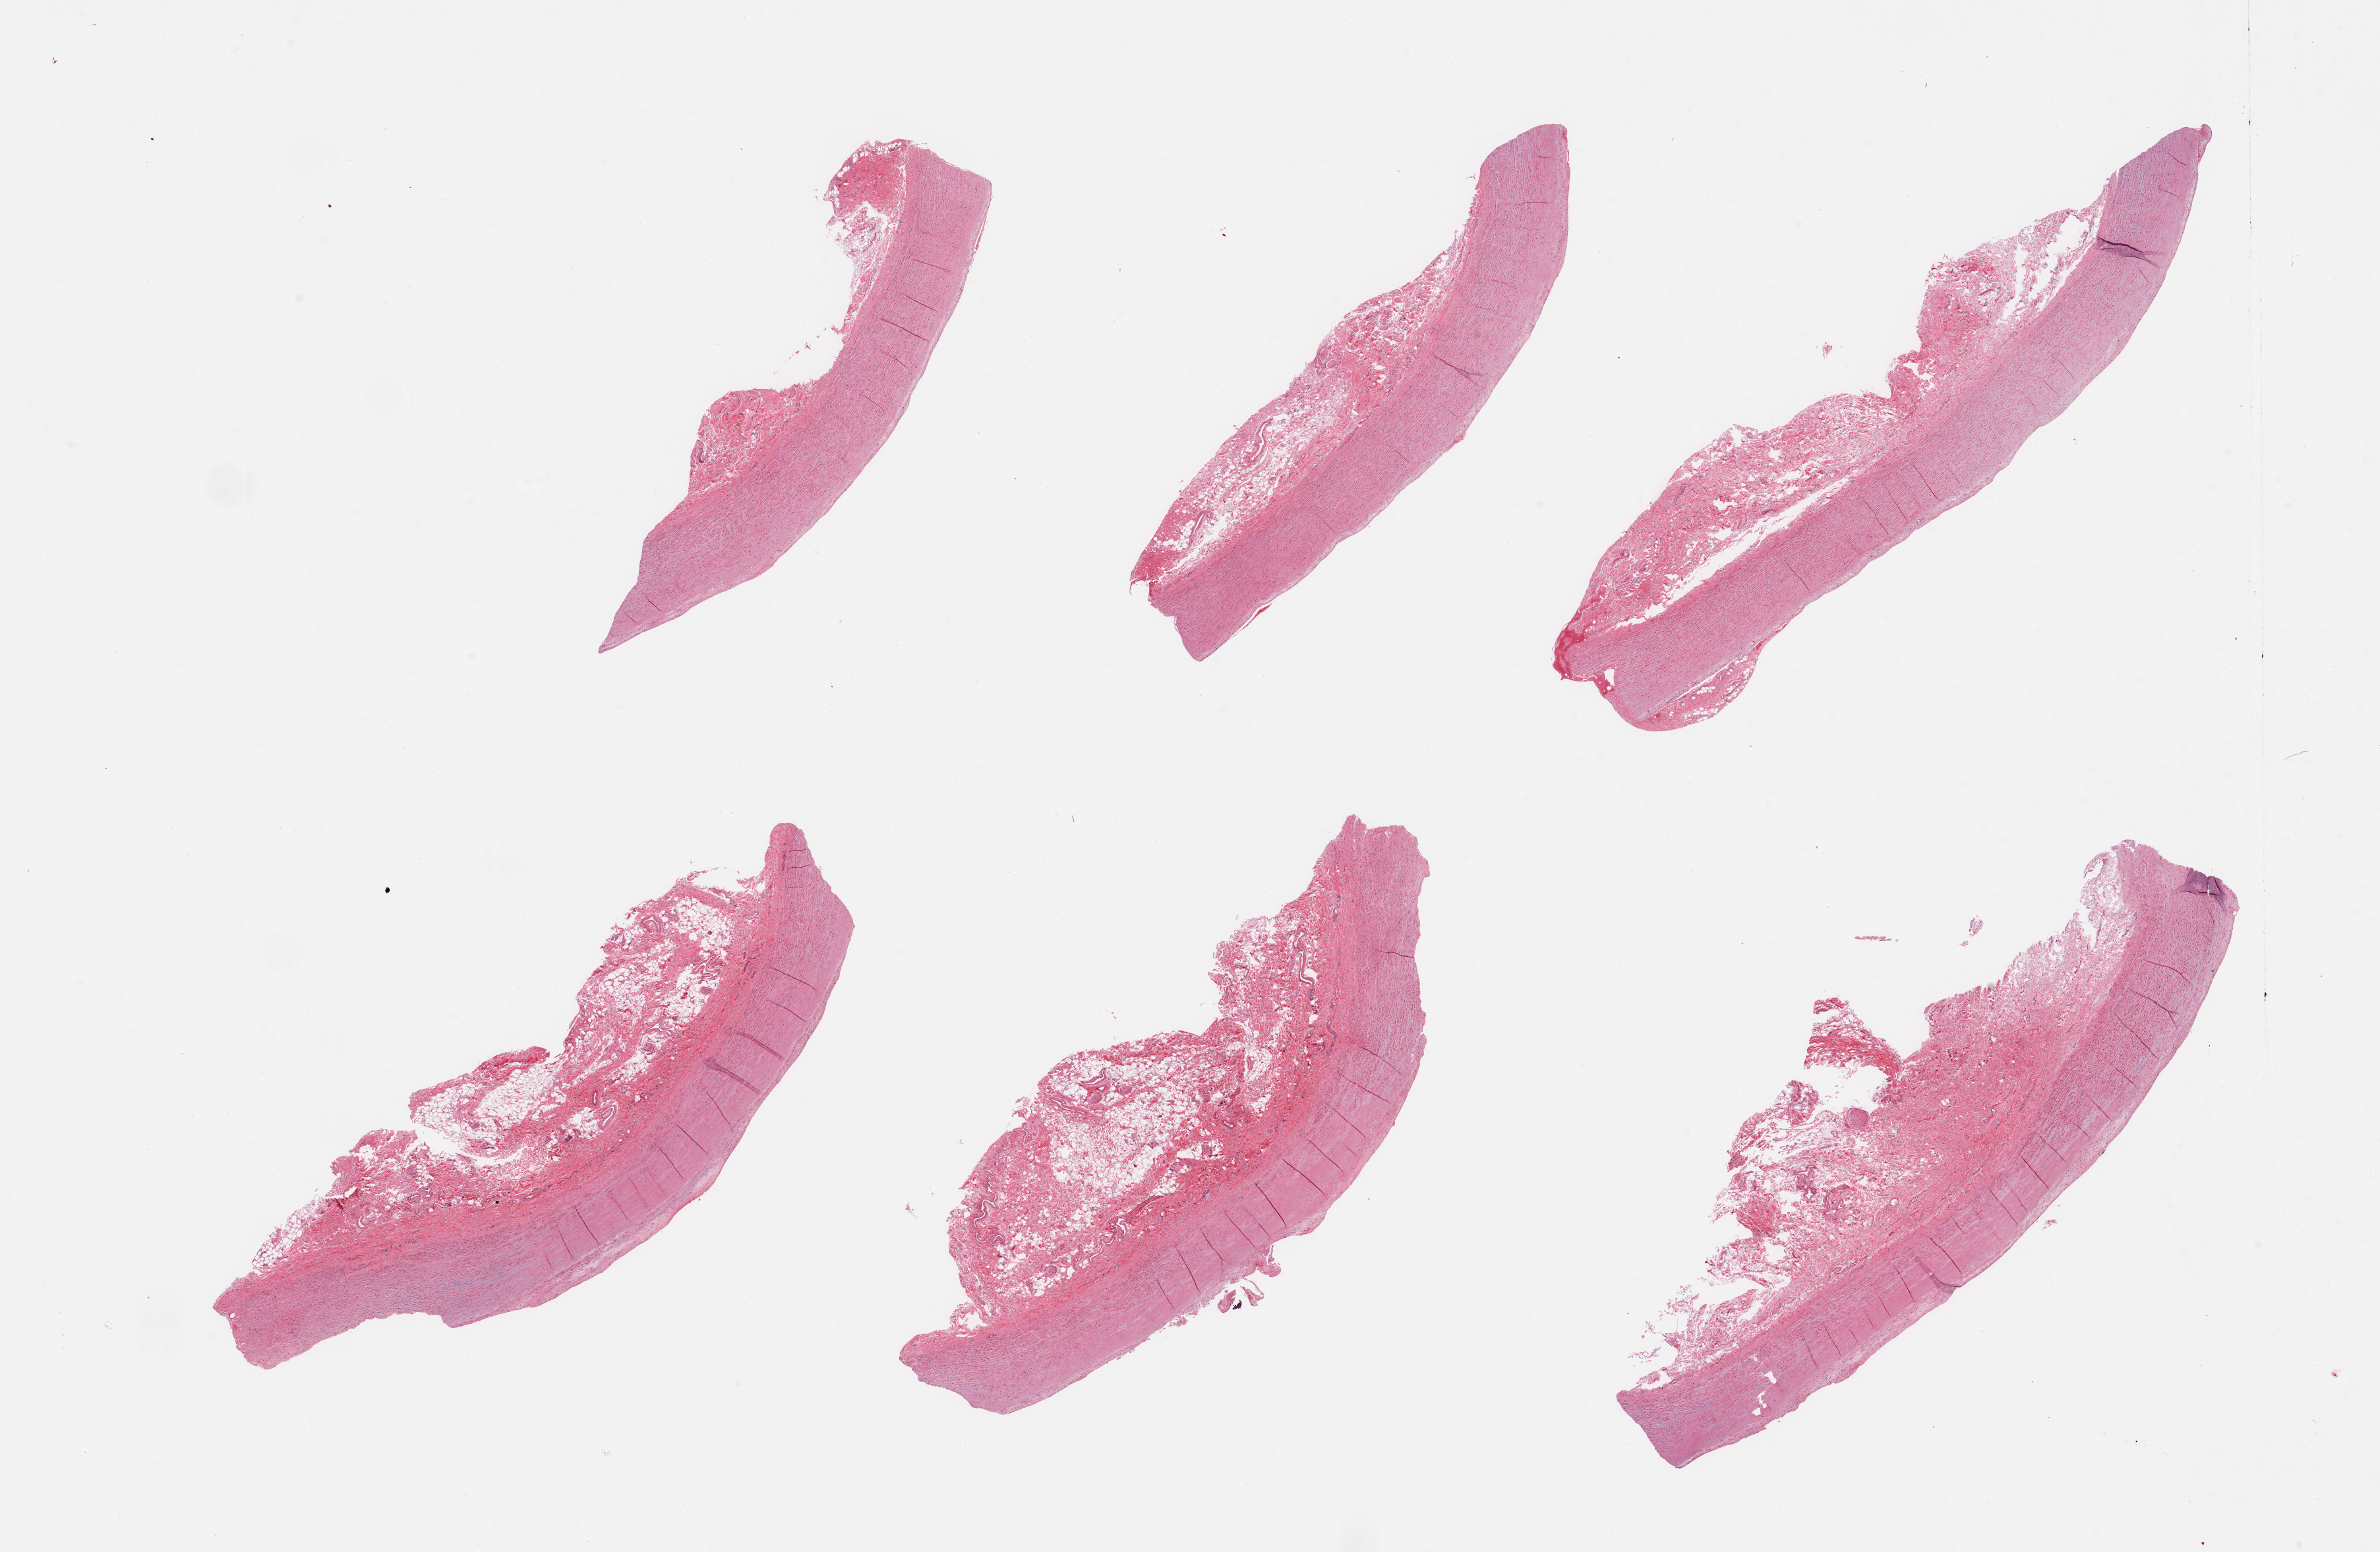
Haematoxylin and eosin whole-slide image — a low-resolution overview of the entire scanned area, about 28.5 x 18.6 mm. PAXgene-fixed paraffin-embedded (PFPE) section. Target tissue: aorta. Donor tissue sample. Donor sex: female.
Review note (as recorded): 6 pieces; focal medial degeneration; untrimmed adventitia up to 2mm thick.